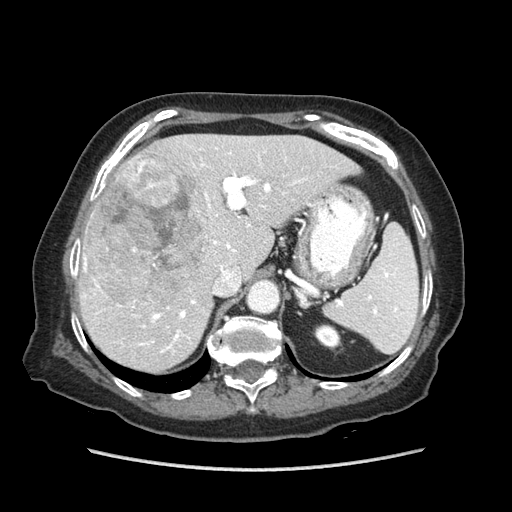
Contrast-enhanced abdominal CT (liver protocol), one axial slice. Soft-tissue window (W 400 / L 40 HU). 512 × 512 image matrix, field of view 360 × 360 mm. From the clinical record (not read from this slice): diagnosis: hepatocellular carcinoma (patient treated with transarterial chemoembolisation; whether this scan precedes or follows treatment is not stated here); TNM stage (as recorded): Stage-IIIA.
Outlined on this slice (semi-automatically segmented with operator editing):
- liver parenchyma outside the tumour (the mass and vessels are separate outlines, so this box may not span the whole liver): box from (x=78, y=134) to (x=360, y=372) px
- mass: (x=85, y=155)–(x=208, y=304)
- liver vessels: (x=83, y=152)–(x=305, y=353)